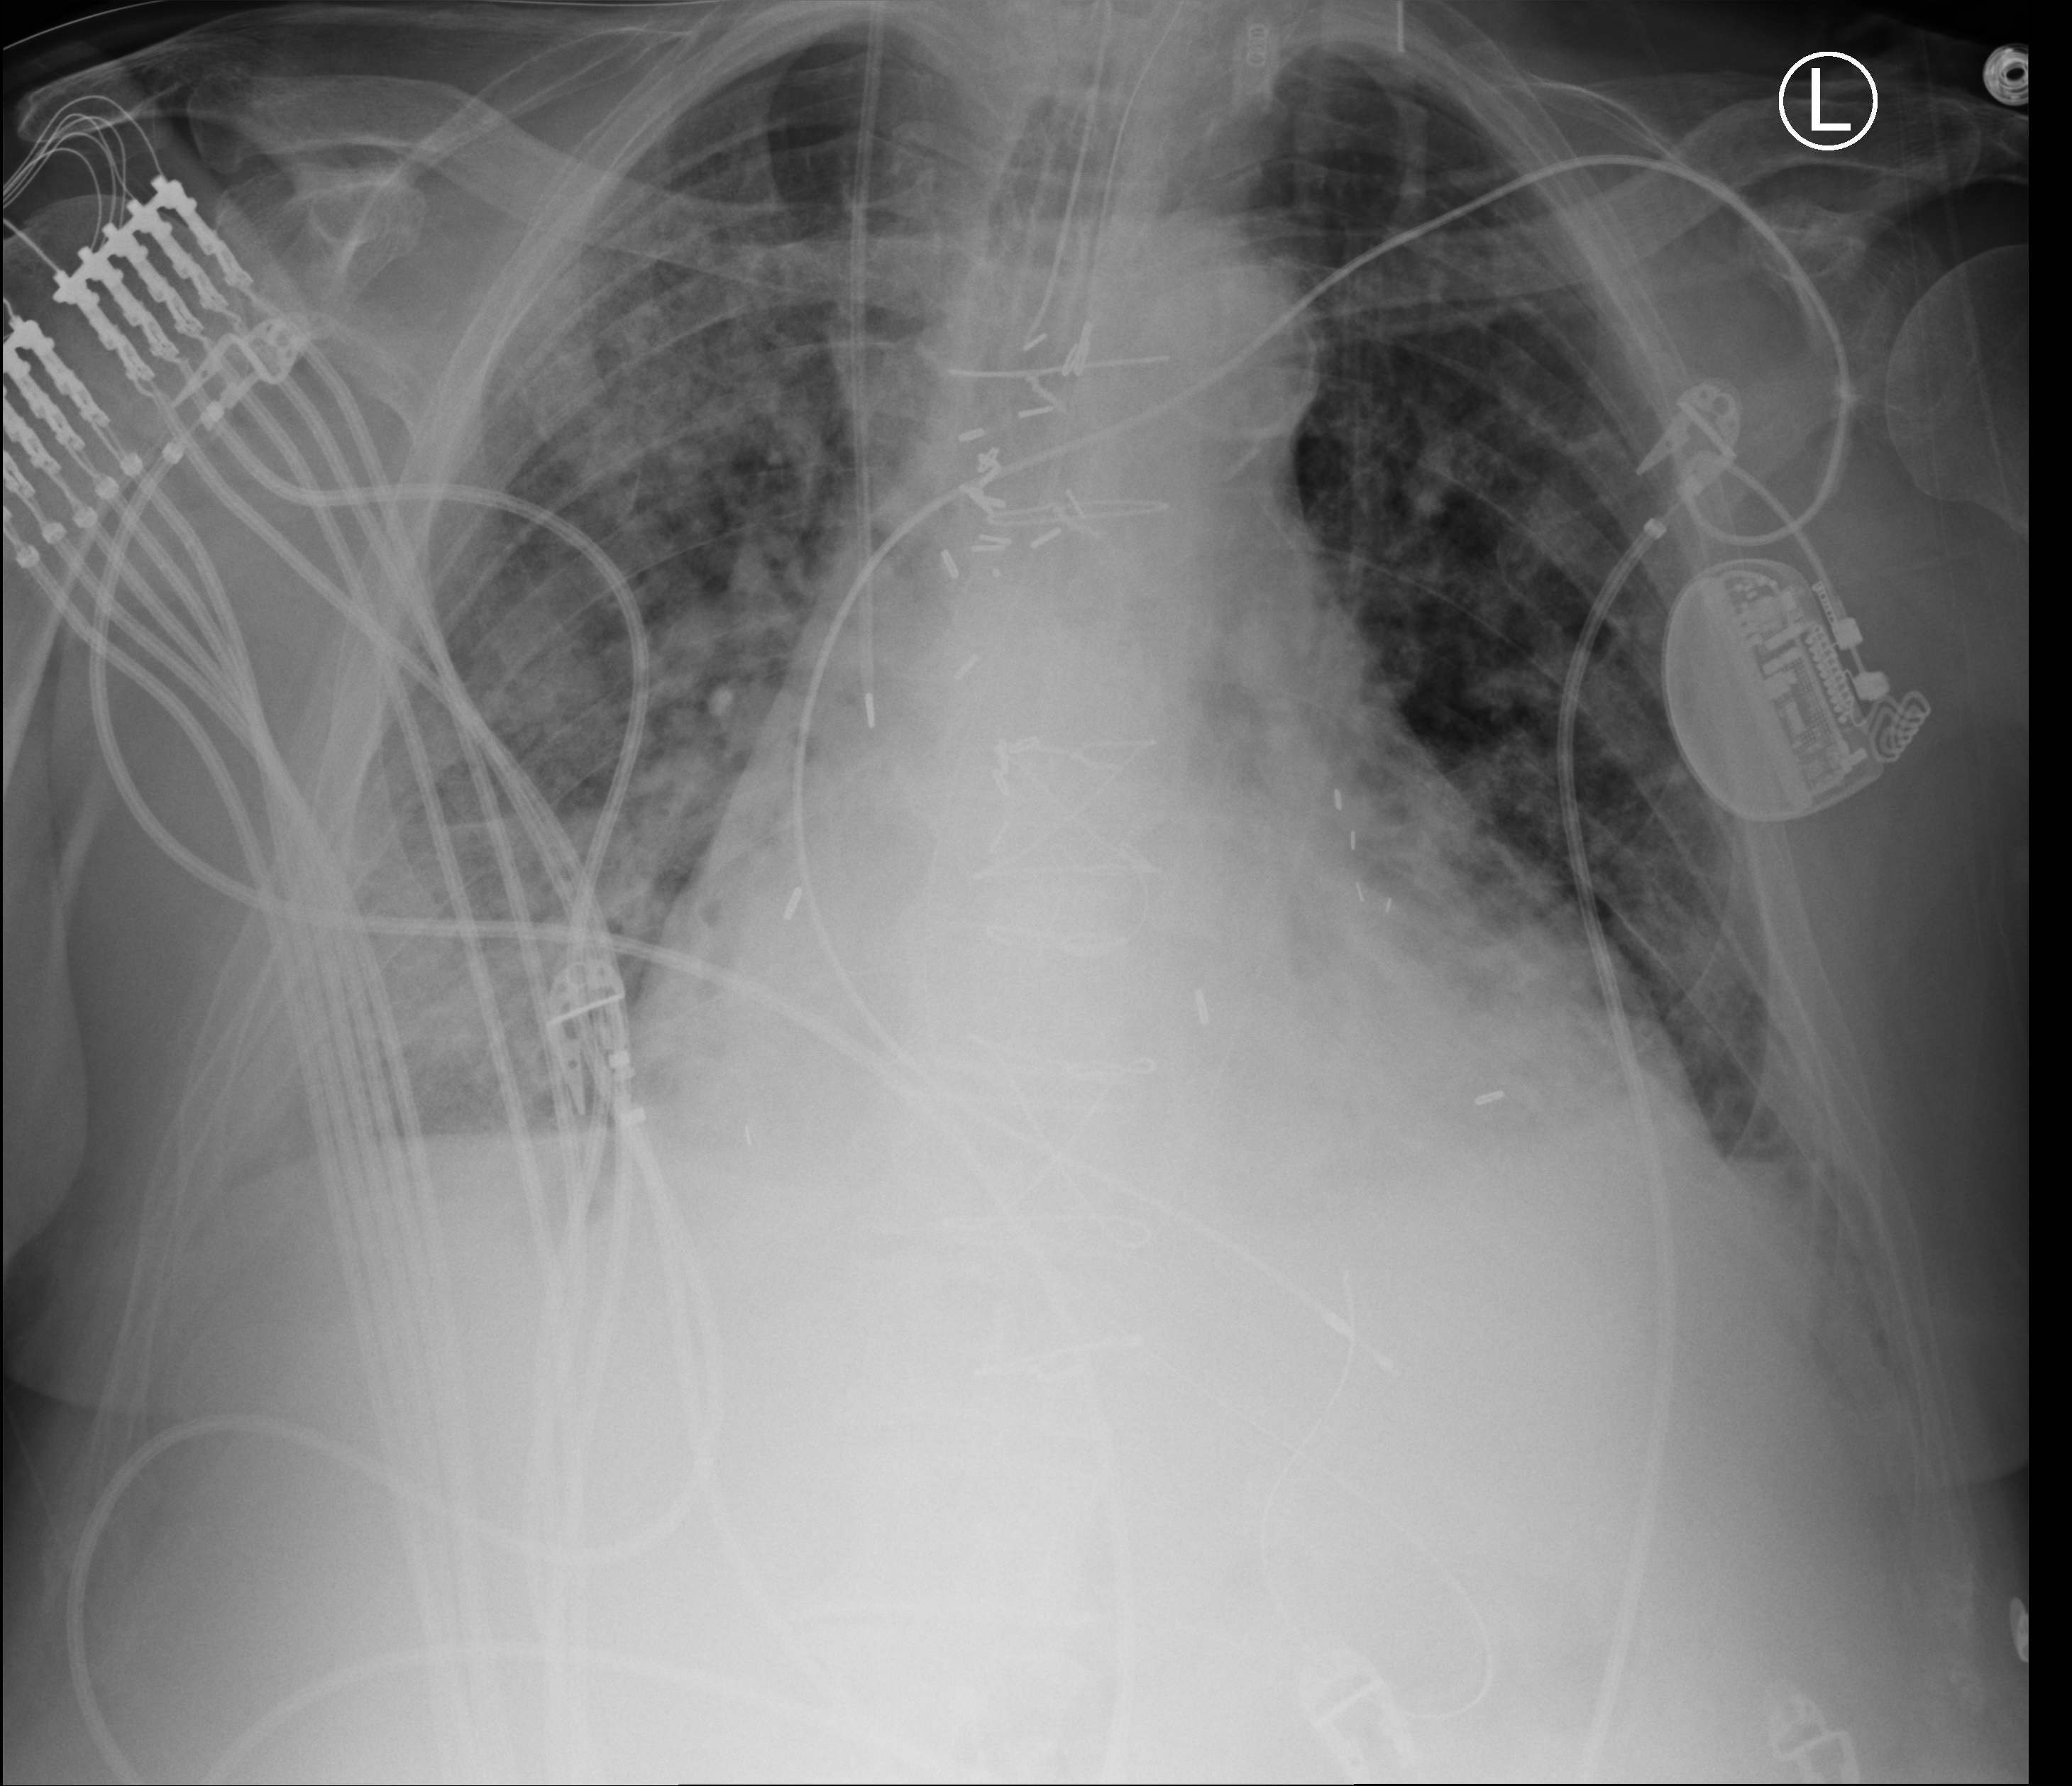
Portable chest radiograph; anteroposterior (AP) projection. Male patient hospitalised with COVID-19, age 75–90 years.
Admission-level facts for this patient (not findings on this image; timing relative to this image not recorded): mechanically ventilated during this hospital stay: yes.